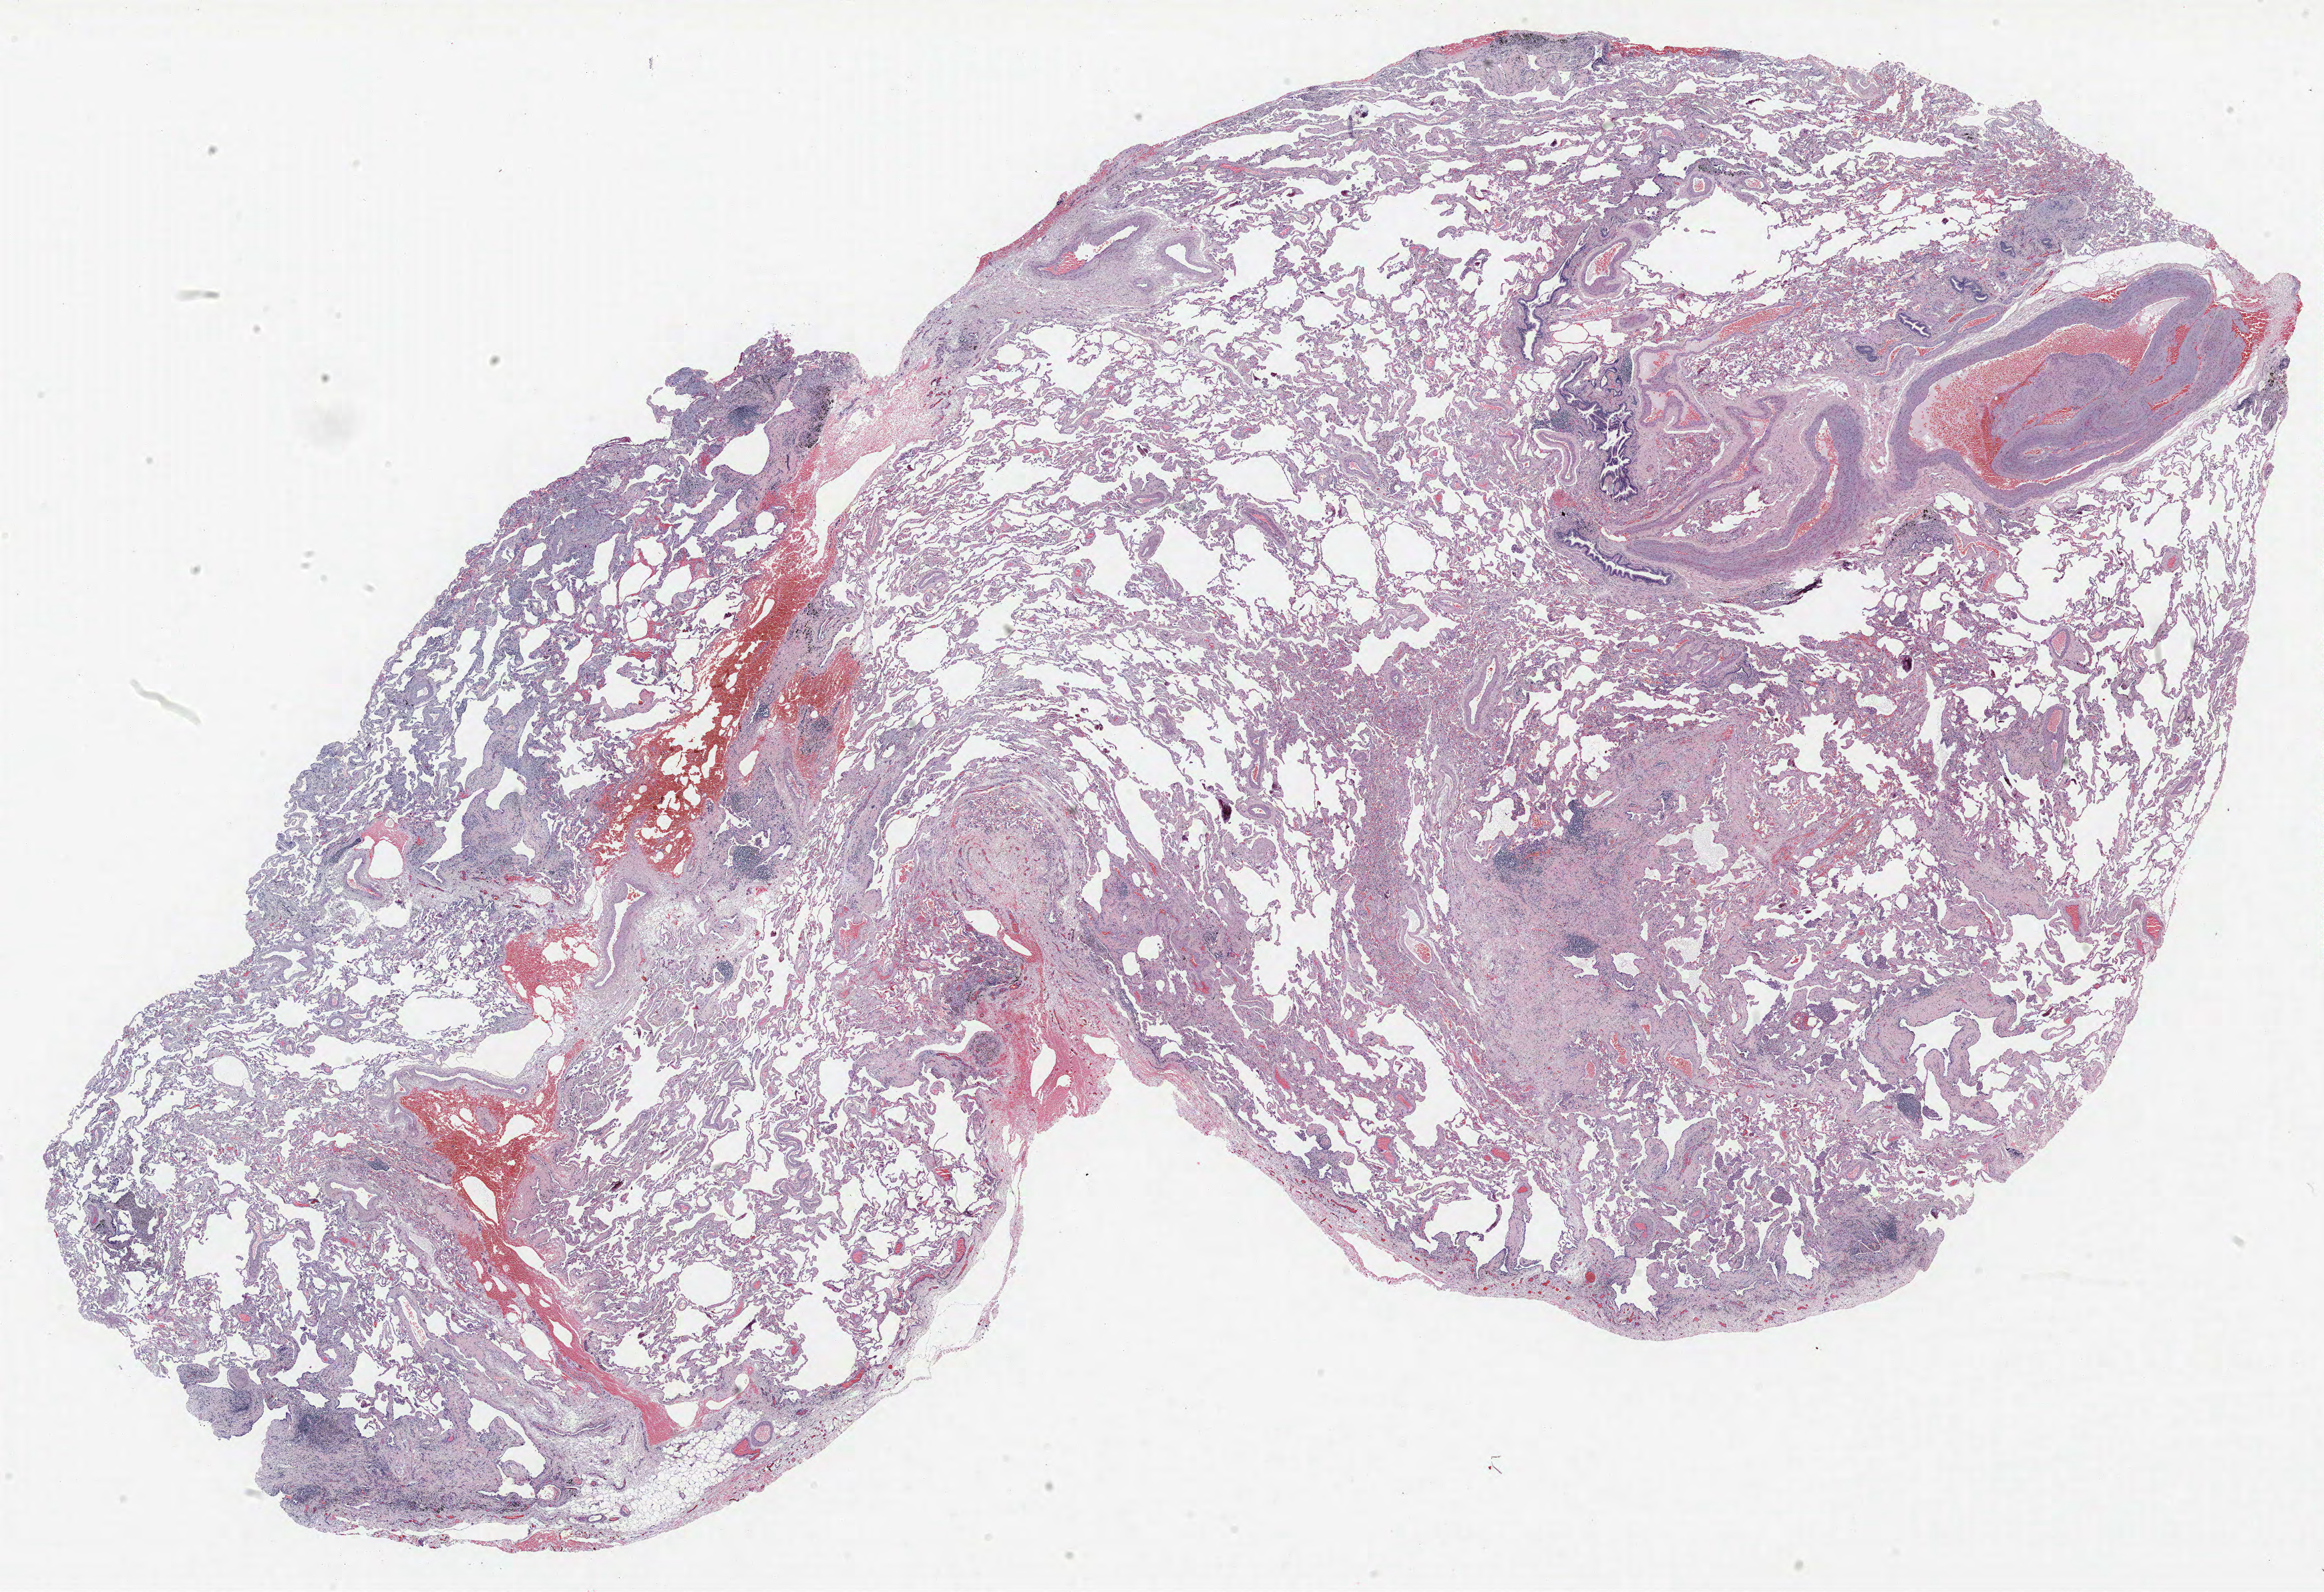
H&E whole-slide image — low-resolution overview of the scanned area, about 27.8 x 19.1 mm (from a 40x scan); FFPE section; lung. Male patient, aged 68 at enrolment. Former smoker at enrolment. Grade: moderately differentiated (G2).
* primary tumour location (clinical record): left upper lobe
* participant's lung-cancer diagnosis: Squamous cell carcinoma, NOS (ICD-O-3 8070/3)
* tumour size (pathology): 17 mm
* stage (AJCC 6th edition): IA